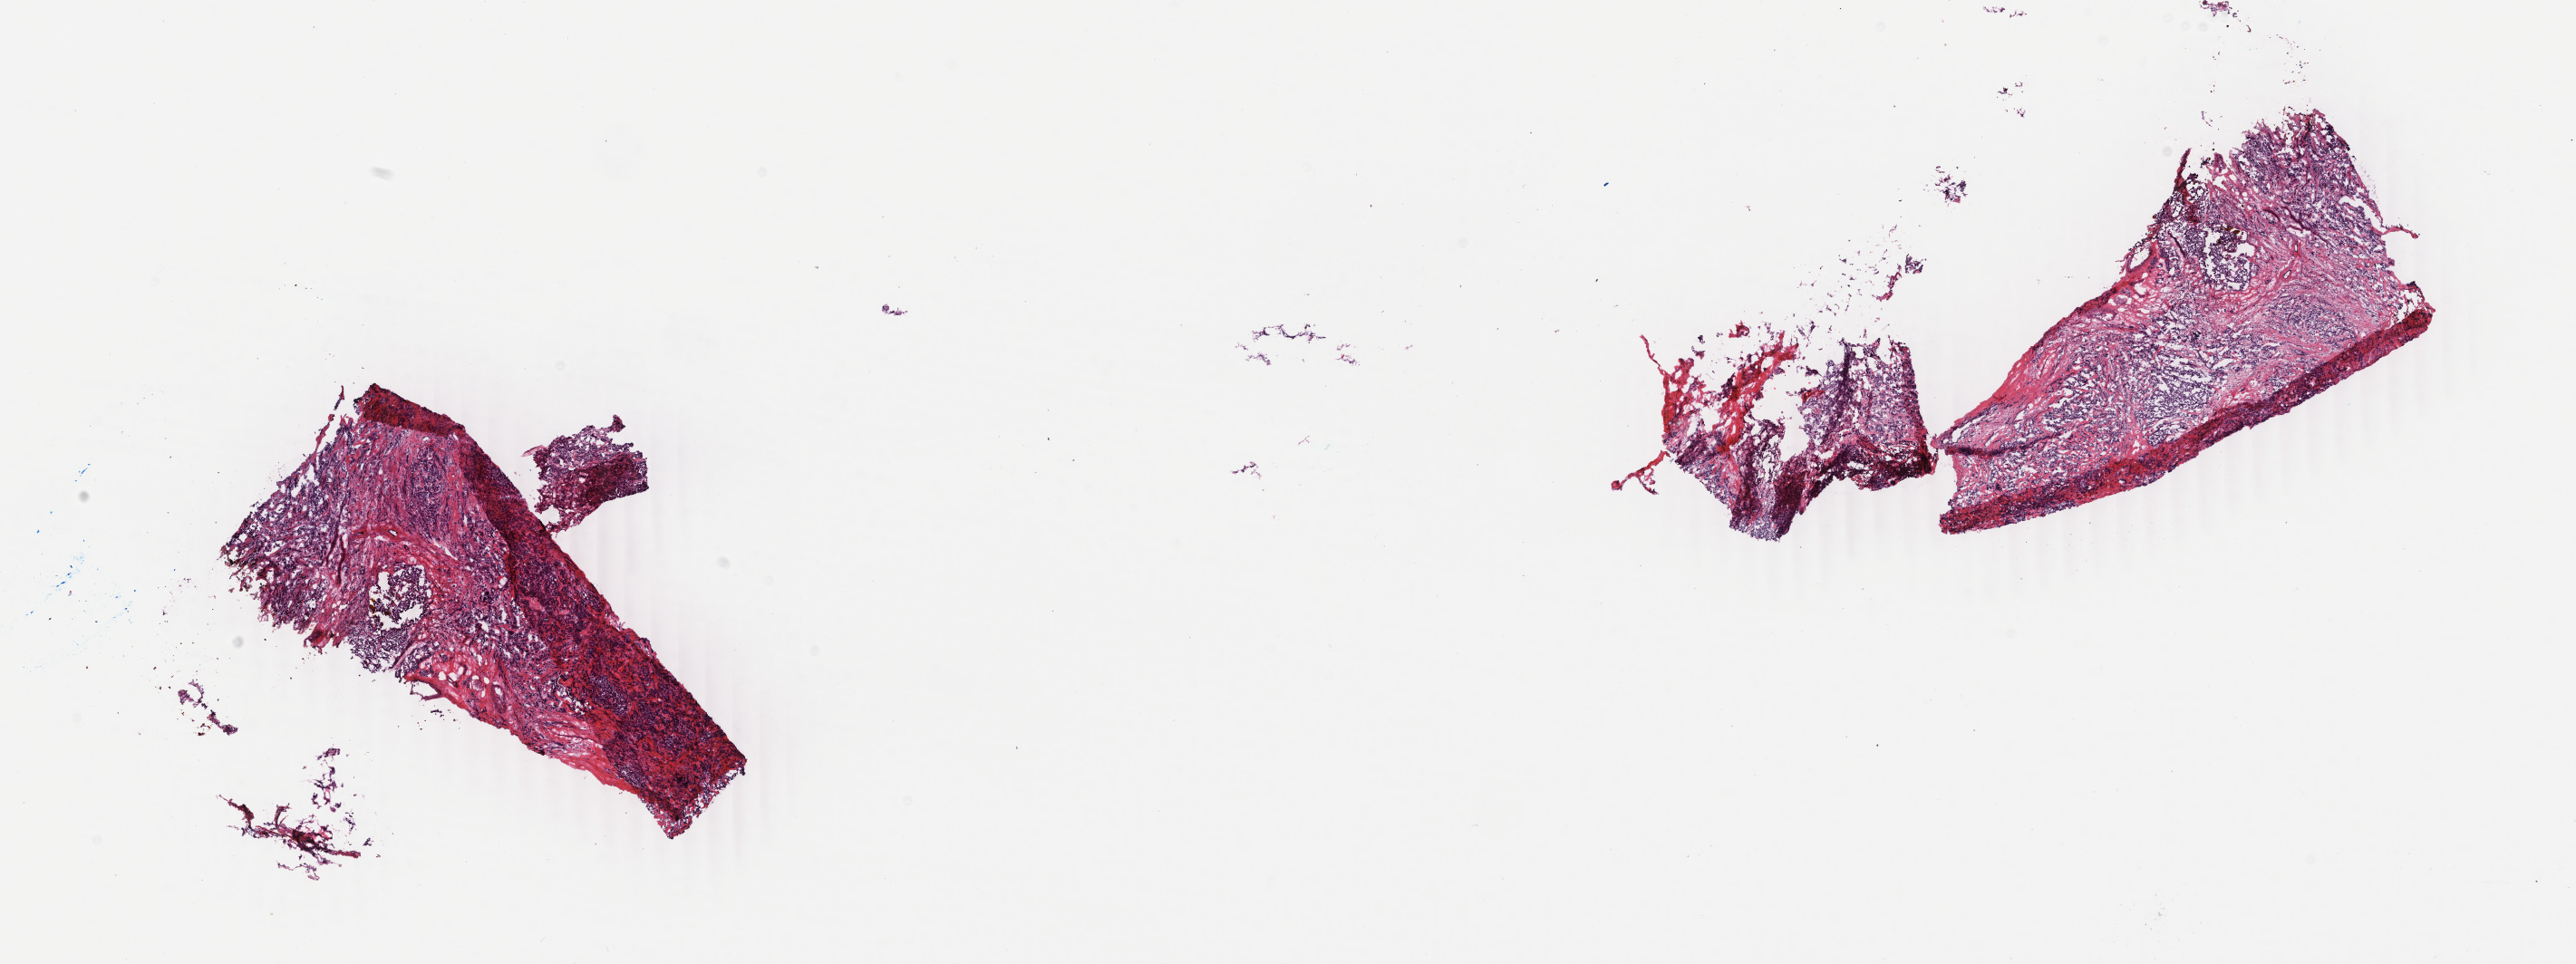
Whole-slide histology image, H&E-stained — low-resolution overview of the scanned area, about 22.6 x 8.5 mm (slide scanned at 40x), frozen section, primary tumour sample from the breast. Female, age 59 years at initial diagnosis. Pathologist review of this section (percent, as recorded): tumour cells 90%, tumour nuclei 75%, normal cells 0%, stromal cells 10%, necrosis 0%. Inflammatory infiltration, as recorded: lymphocyte infiltration 0%, monocyte infiltration 0%, neutrophil infiltration 0%.
• AJCC pathologic stage: IIB
• diagnosis: Infiltrating duct carcinoma, NOS
• laterality: right